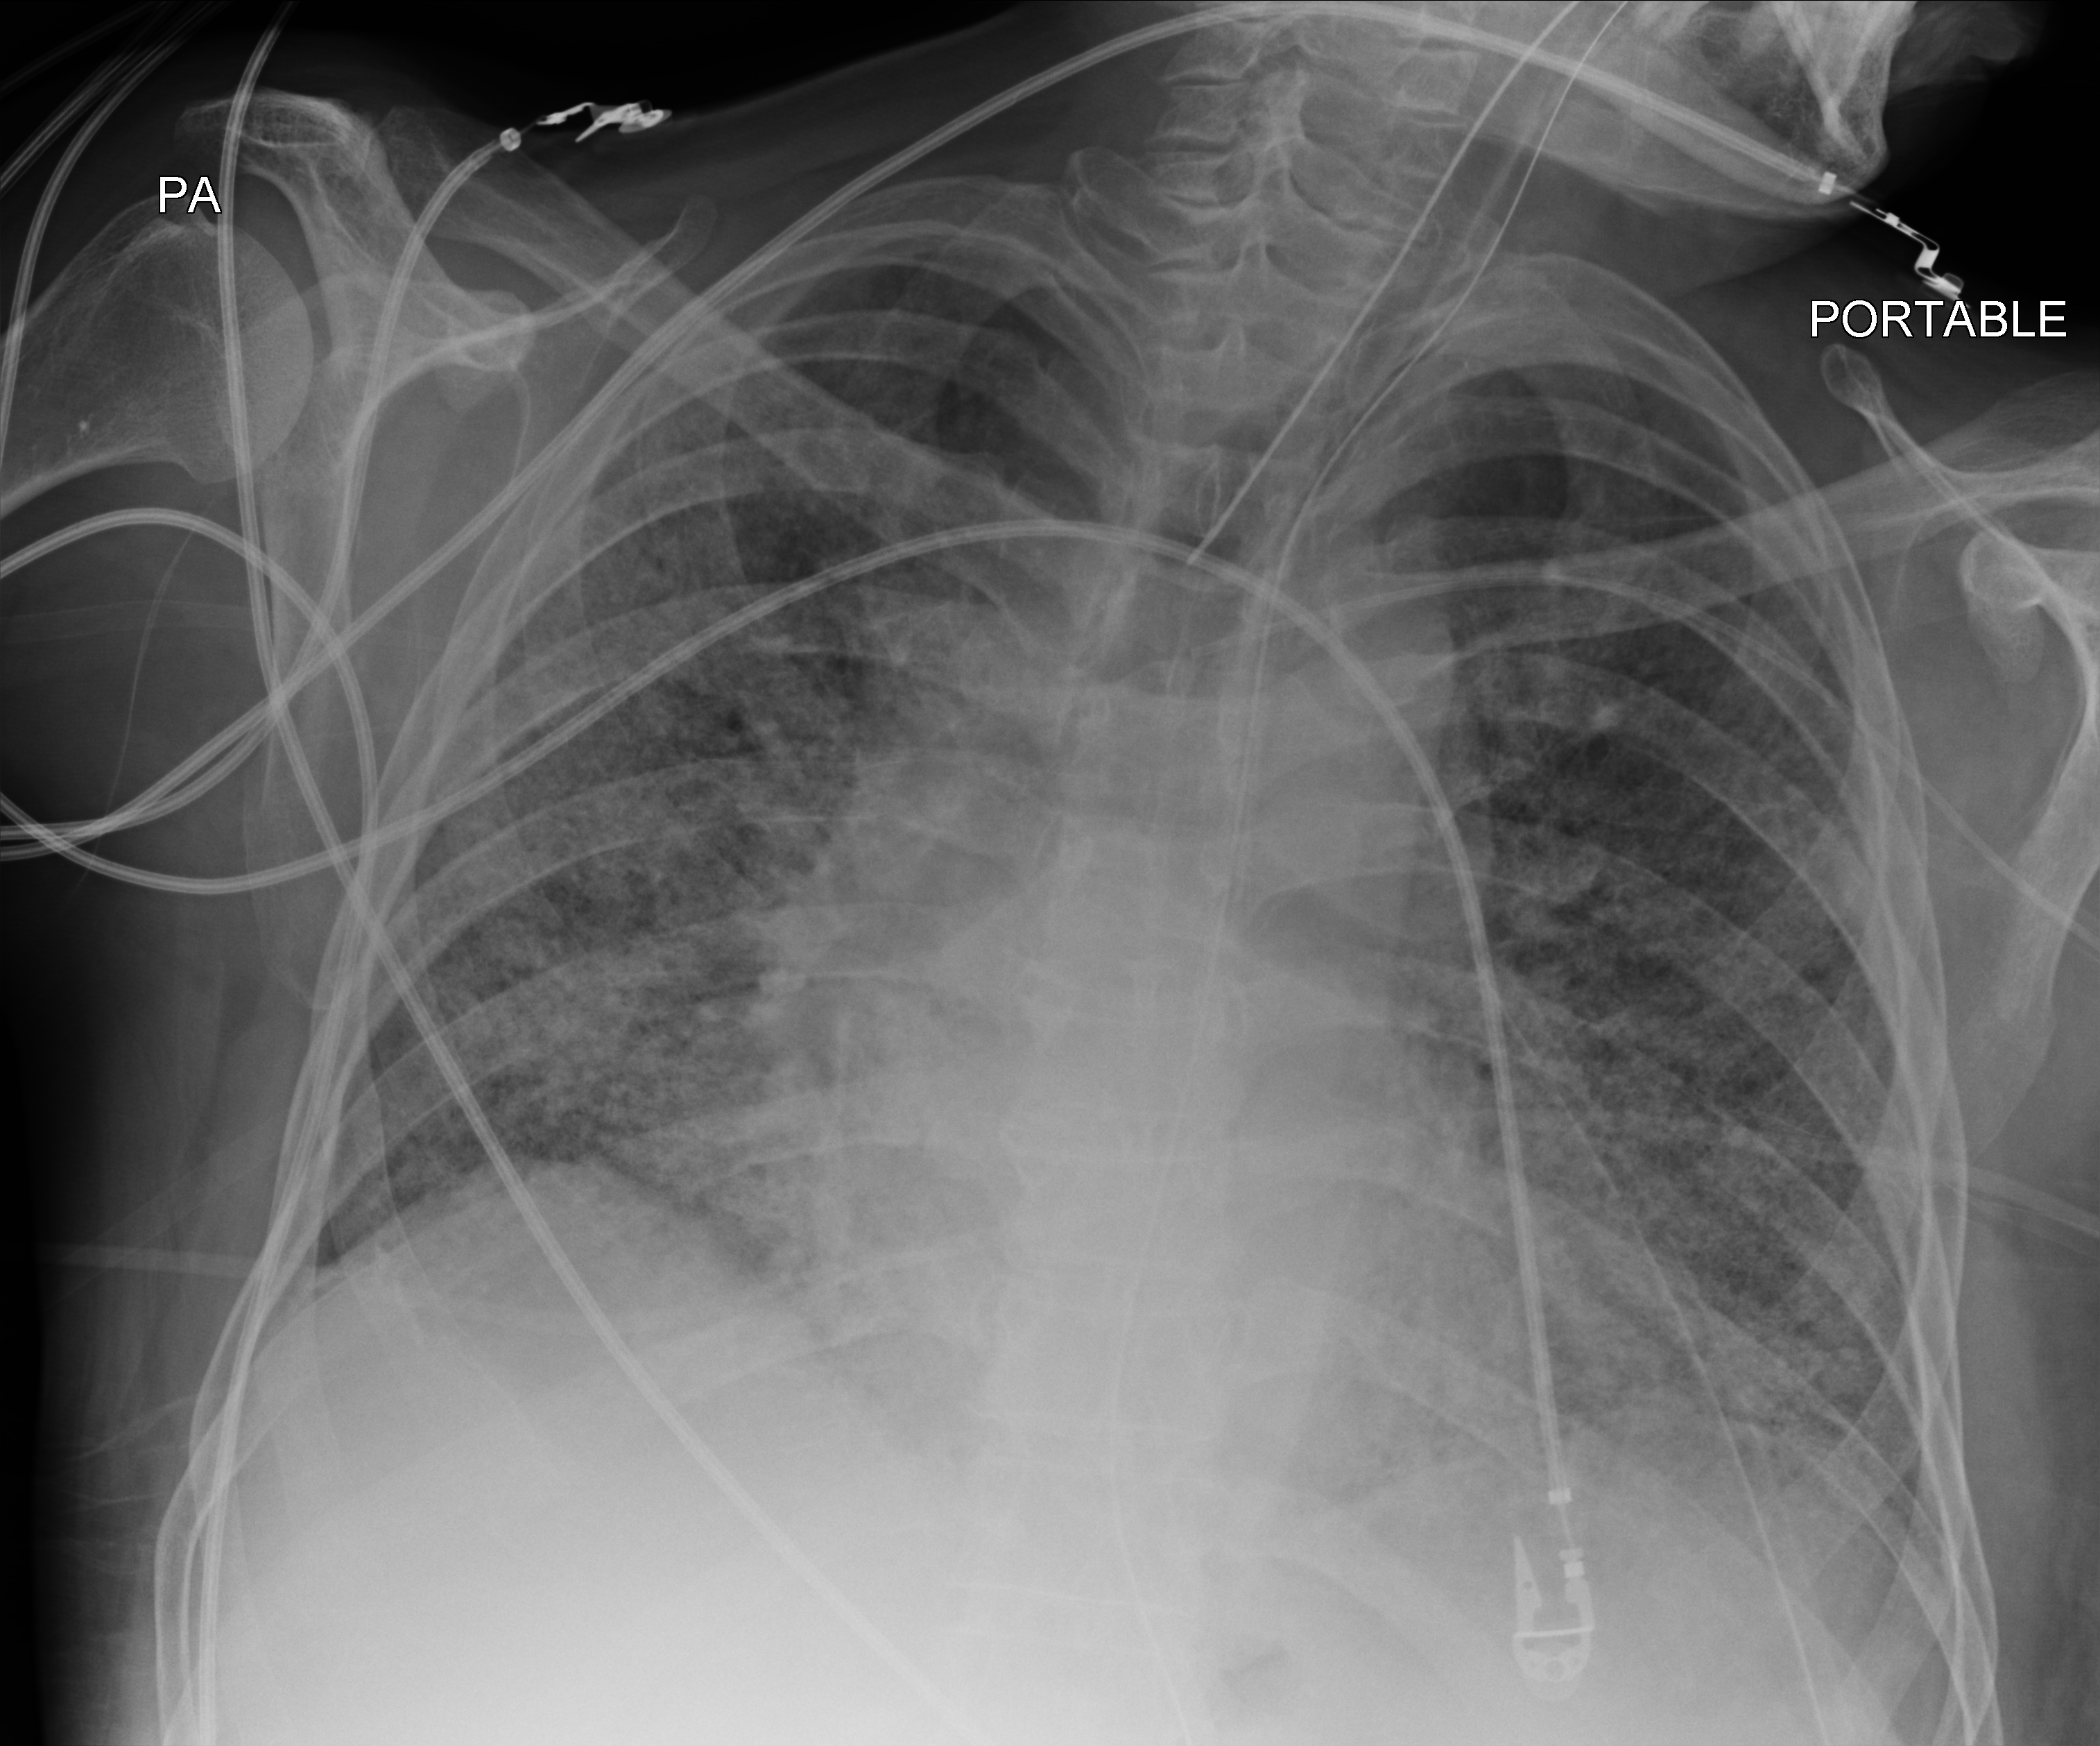
Portable chest radiograph. Male patient hospitalised with COVID-19, age 60–74 years.
Hospital-stay facts (about this admission, not read from this image; timing relative to this image not recorded):
- mechanically ventilated during this hospital stay: yes
- admitted to intensive care during this hospital stay: yes